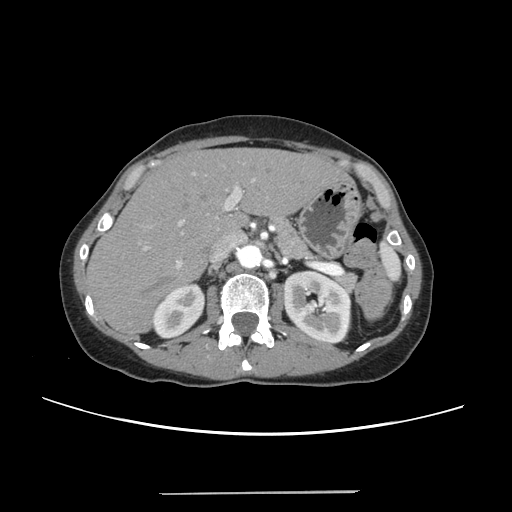
Contrast-enhanced abdominal CT, one axial slice; slice 155 of 240 in the series (ordered by position); 120 kVp; intravenous contrast given; soft-tissue window (W 400 / L 40 HU); 512 × 512 image matrix, field of view 371 × 371 mm. Female patient, age 60 years. Case-level facts recorded for this patient, not image findings: diagnosis: colorectal cancer liver metastases, imaged before liver resection.
Outlined on this slice (outlined manually by an expert reader):
- liver: bounding box [x1, y1, x2, y2] px = [89, 149, 346, 332]
- planned liver remnant (the part of the liver to remain after resection): [89, 149, 345, 332]
- portal vein (with intrahepatic branches): [140, 171, 257, 267]